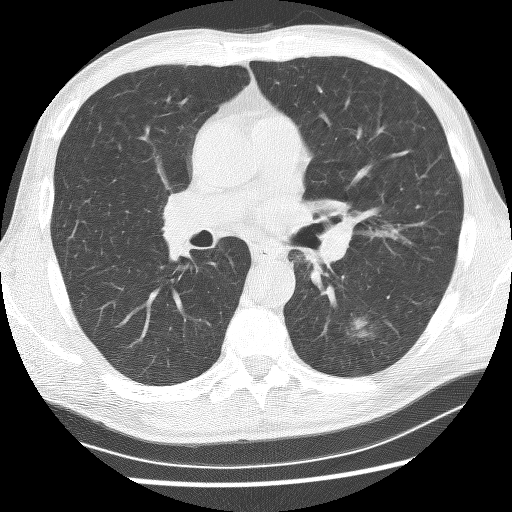
Low-dose screening chest CT, one axial slice; slice 139 of 253 in the series (ordered by position); 120 kVp; lung window (W 1500 / L -600 HU); 2.5 mm slice thickness; 512 × 512 image matrix, field of view 340 × 340 mm.
Outlined on this slice (outlined manually by an expert reader):
- lesion 1 (tumor, lower lobe of left lung): bounding box [x1, y1, x2, y2] px = [354, 319, 367, 336]